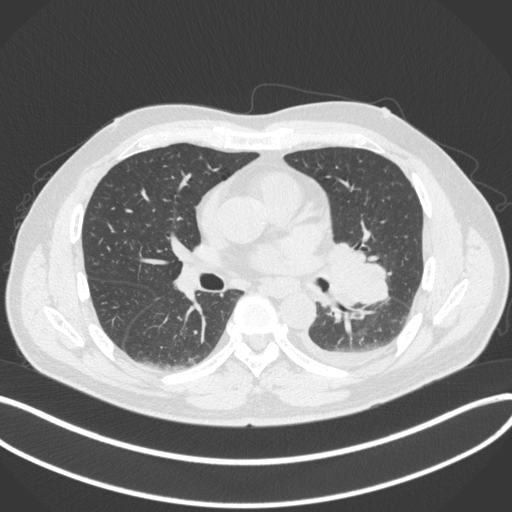
Chest CT, one axial slice; position 190 of 350 along the scan axis; reconstruction kernel B31f; 120 kVp; lung window (W 1500 / L -600 HU); 1 mm slice thickness; 512 × 512 image matrix, field of view 400 × 400 mm. Patient: male, 58 years. Case-level facts recorded for this patient, not image findings: clinical TNM (as recorded): T3 N1 M1b; histopathological grade: G3.
Structures marked on this image (rectangle marked by the reading radiologist):
- lung tumour (recorded histology: small cell carcinoma): bounding box <321,236,396,311> (left, top, right, bottom; pixels)